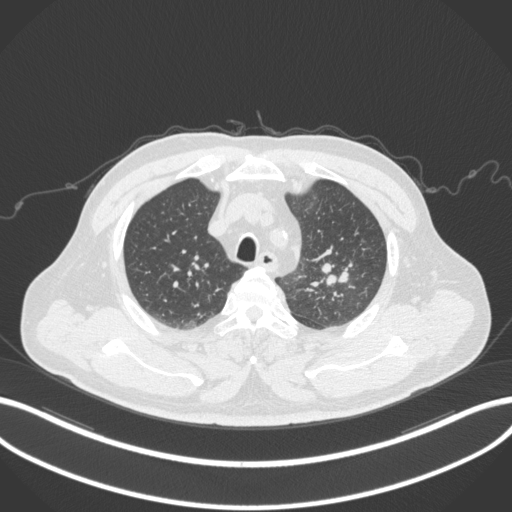
Chest CT, one axial slice; position 241 of 286 along the scan axis; reconstruction kernel B31f; 120 kVp; lung window (W 1500 / L -600 HU); 1 mm slice thickness; 512 × 512 image matrix. Male patient, age 67 years. From the clinical record (not read from this slice): clinical TNM (as recorded): T2a N1 M0; histopathological grade: G3.
Annotated regions visible in this slice (rectangle marked by the reading radiologist):
- lung tumour (recorded histology: adenocarcinoma): bounding box <322,261,350,289> (left, top, right, bottom; pixels)